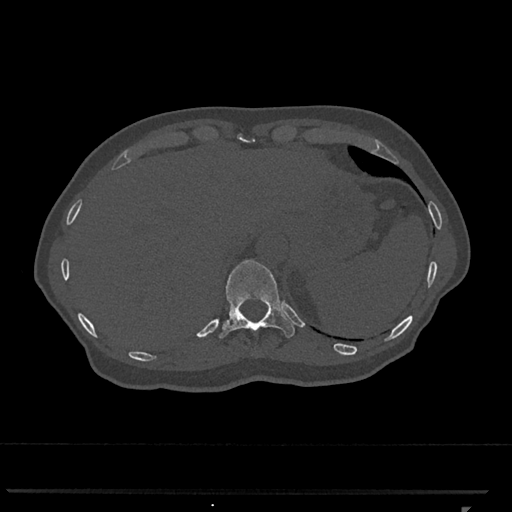
CT including the spine, one axial slice; slice 523 of 793 in the series (ordered by position); reconstruction kernel Br40s/3; 120 kVp; bone window (W 1800 / L 400 HU); 512 × 512 image matrix, field of view 380 × 380 mm. Female patient, age 62 years. From the clinical record (not read from this slice): primary cancer: renal.
Structures marked on this image (semi-automatic segmentation, software-assisted and operator-edited):
- T11 vertebra: bounding box <219,259,295,338> (left, top, right, bottom; pixels)